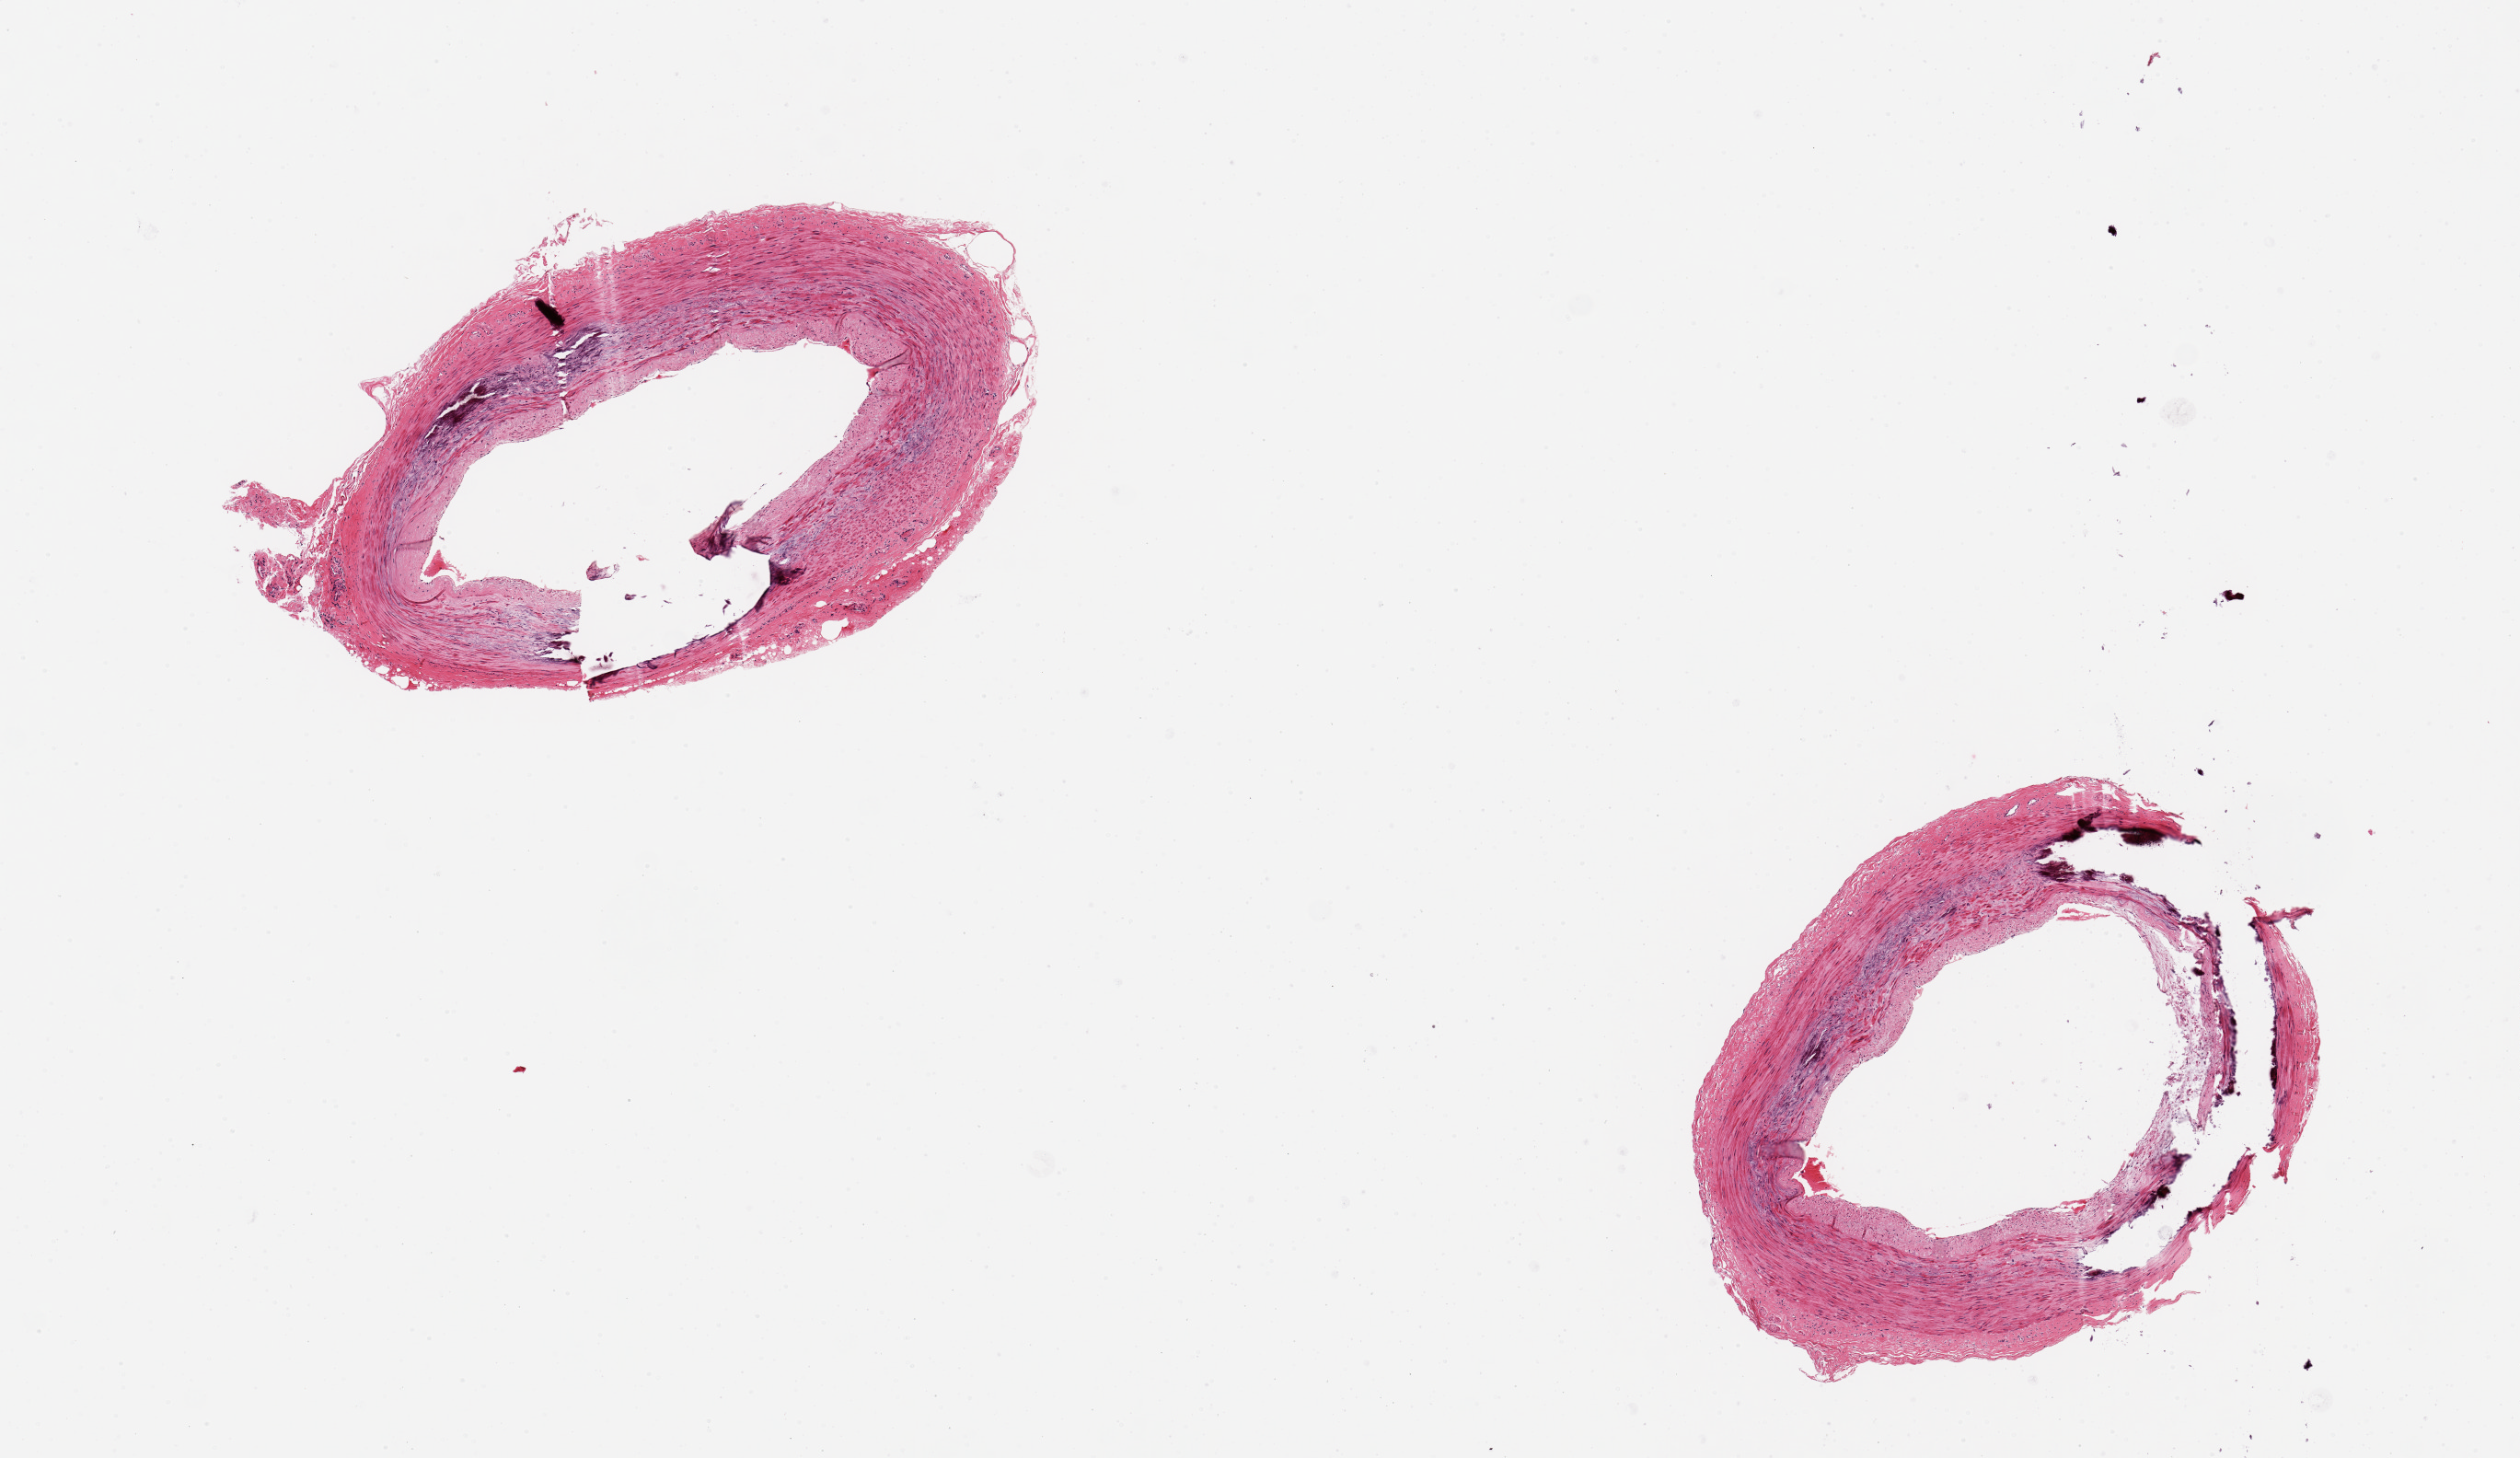
Haematoxylin and eosin whole-slide image, whole scanned area (about 10.8 x 6.3 mm, from a 20x scan) shown as a low-resolution overview. PAXgene-fixed paraffin-embedded (PFPE) section. Sampled site (target tissue): tibial artery. Donor tissue sample. Donor: male.
- review note (as recorded): 2 aliquots, ~2.5mm d; Monckeberg's sclerosis noted